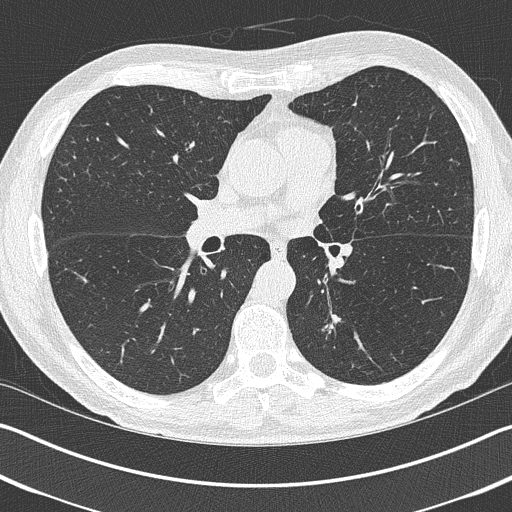
Chest CT (low-dose screening protocol), one axial image; baseline annual screen; lung window (W 1500 / L -600 HU); lung (sharp) reconstruction kernel (B50f); slice 178 of 402 in the series; 512 × 512 image matrix, field of view 340 × 340 mm. Male, age 69 years at enrolment. Current smoker at enrolment.
• Expert-annotated lung lesion, bounding box <293,304,350,363> (left, top, right, bottom; pixels).
• Reader record for this screening exam (exam-level; its link to the box is not recorded): non-calcified nodule or mass ≥4 mm, left upper lobe, 19 × 19 mm, spiculated (stellate) margins, pre-existing on the prior screen: yes.
• Official screen result: positive, change unspecified: nodule(s) >= 4 mm or enlarging nodule(s), mass(es), or other non-specific abnormalities suspicious for lung cancer.
• Participant outcome: lung cancer diagnosed 202 days after this screen — non-small cell carcinoma, left lower lobe, stage IIIA (AJCC 6th edition), 20 mm at pathology.